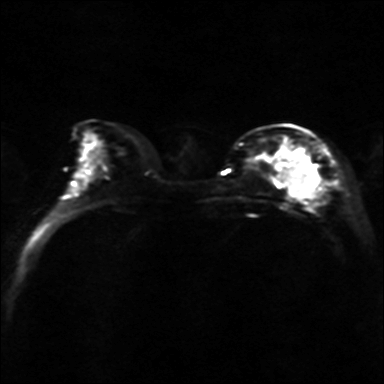
Breast MRI, one axial slice. Position 15 of 36 along the scan axis. Diffusion-weighted series; image 2 of 4 stored at this slice position (different b-values; order by instance number). 3 T. 4 mm slice thickness. 384 × 384 image matrix. Female patient.
Structures marked on this image (outlined manually by an expert reader):
- tumour on diffusion-weighted imaging: box from (x=285, y=156) to (x=319, y=199) px